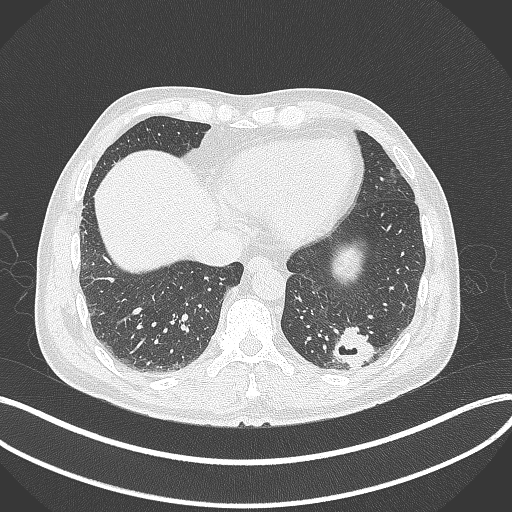
Chest CT, one axial slice. Slice 70 of 300 in the series (ordered by position). Reconstruction kernel B70f. Lung window (W 1500 / L -600 HU). 1 mm slice thickness. 512 × 512 image matrix, field of view 400 × 400 mm. Patient: male, 54 years. Case-level facts recorded for this patient, not image findings: clinical TNM (as recorded): T1c N0 M1.
Structures marked on this image (bounding box drawn by a radiologist):
- lung tumour (recorded histology: adenocarcinoma): bounding box <330,324,375,370> (left, top, right, bottom; pixels)